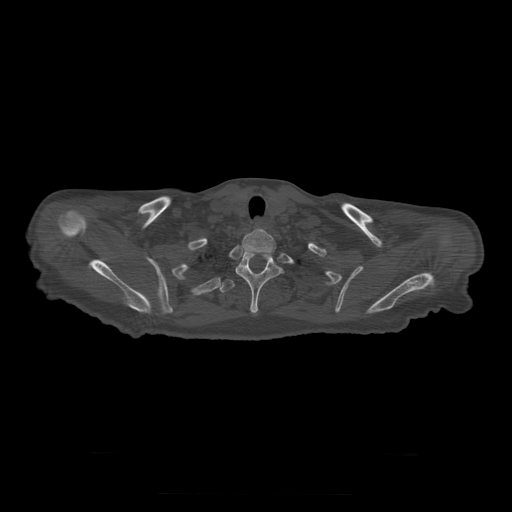
CT including the spine, one axial slice; reconstruction kernel STANDARD; bone window (W 1800 / L 400 HU); 512 × 512 image matrix, field of view 510 × 510 mm. Patient age 73 years. From the clinical record (not read from this slice): primary cancer: prostate.
Structures marked on this image (semi-automatic segmentation, software-assisted and operator-edited):
- T1 vertebra: bounding box (x1, y1, x2, y2) in pixels: (242, 231, 276, 254)
- T2 vertebra: (236, 252, 284, 314)
- T3 vertebra: (220, 280, 236, 293)